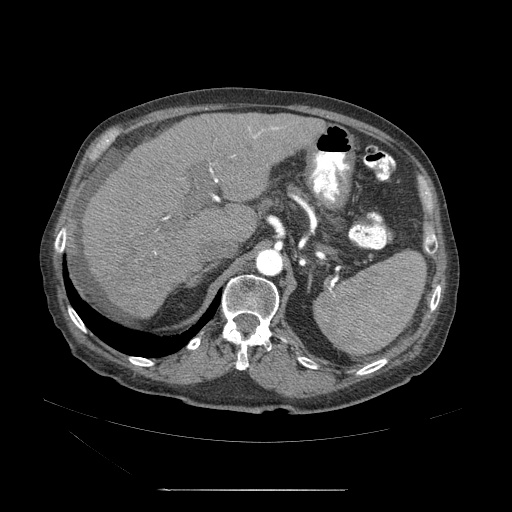
Contrast-enhanced abdominal CT (liver protocol), one axial slice; slice 31 of 71 in the series (ordered by position); reconstruction kernel STANDARD; 120 kVp; soft-tissue window (W 400 / L 40 HU); 2.5 mm slice thickness; 512 × 512 image matrix, field of view 440 × 440 mm. From the clinical record (not read from this slice): diagnosis: hepatocellular carcinoma (patient treated with transarterial chemoembolisation; whether this scan precedes or follows treatment is not stated here); TNM stage (as recorded): Stage-II; Child-Pugh class: A.
Annotated regions visible in this slice (semi-automatic segmentation, software-assisted and operator-edited):
- abdominal aorta: bounding box (x1, y1, x2, y2) in pixels: (257, 247, 284, 277)
- liver parenchyma outside the tumour (the mass and vessels are separate outlines, so this box may not span the whole liver): (80, 113, 325, 322)
- liver vessels: (128, 159, 238, 287)